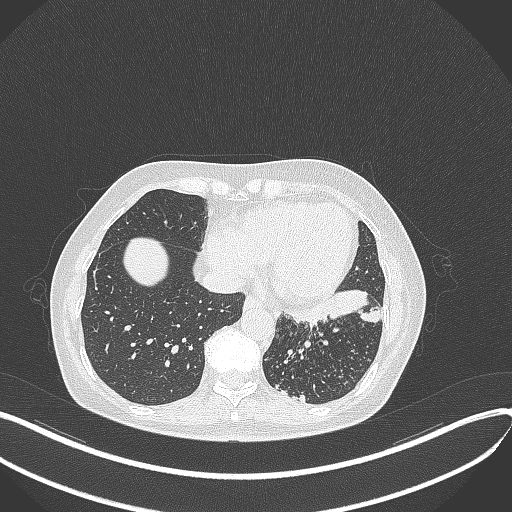
Chest CT, one axial slice; position 123 of 429 along the scan axis; reconstruction kernel B70f; lung window (W 1500 / L -600 HU); 1 mm slice thickness; 512 × 512 image matrix, field of view 400 × 400 mm. Female patient, age 63 years. Case-level facts recorded for this patient, not image findings: clinical TNM (as recorded): T1b N0 M0.
Annotated regions visible in this slice (bounding box drawn by a radiologist):
- lung tumour (recorded histology: adenocarcinoma): bounding box <284,285,386,332> (left, top, right, bottom; pixels)